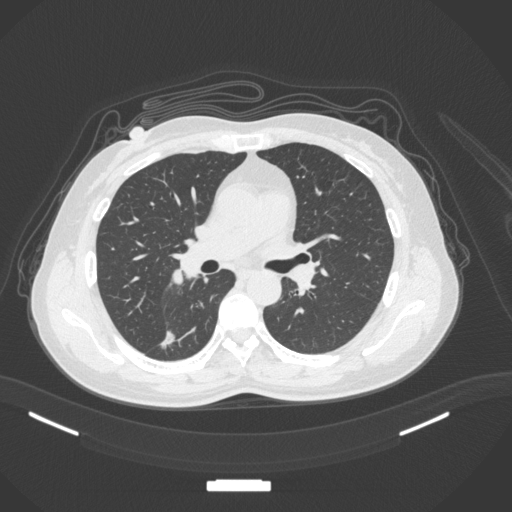
Chest CT, one axial slice. Position 177 of 352 along the scan axis. Reconstruction kernel B31f. 120 kVp. Lung window (W 1500 / L -600 HU). 1 mm slice thickness. 512 × 512 image matrix, field of view 400 × 400 mm. Female patient, age 55 years. Case-level facts recorded for this patient, not image findings: clinical TNM (as recorded): T1c N1 M0.
Annotated regions visible in this slice (rectangle marked by the reading radiologist):
- lung tumour (recorded histology: adenocarcinoma): bounding box (x1, y1, x2, y2) in pixels: (156, 326, 183, 354)